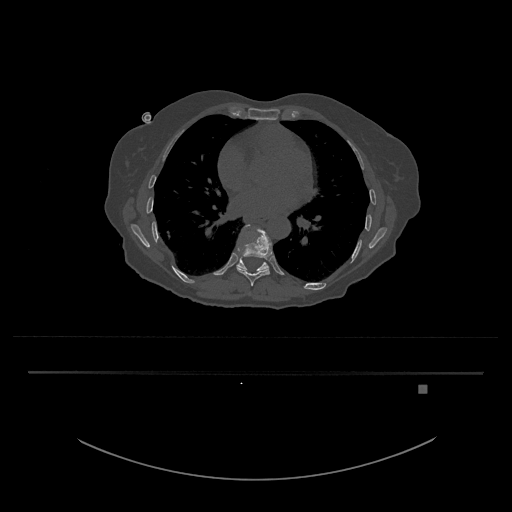
CT including the spine, one axial slice. Slice 745 of 797 in the series (ordered by position). Reconstruction kernel Br40s/3. 120 kVp. Bone window (W 1800 / L 400 HU). 0.5 mm slice thickness. 512 × 512 image matrix, field of view 500 × 500 mm. Patient: female, 57 years. From the clinical record (not read from this slice): primary cancer: cervical.
Annotated regions visible in this slice (semi-automatic segmentation, software-assisted and operator-edited):
- T10 vertebra: bounding box (x1, y1, x2, y2) in pixels: (236, 257, 269, 273)
- T9 vertebra: (237, 225, 272, 286)